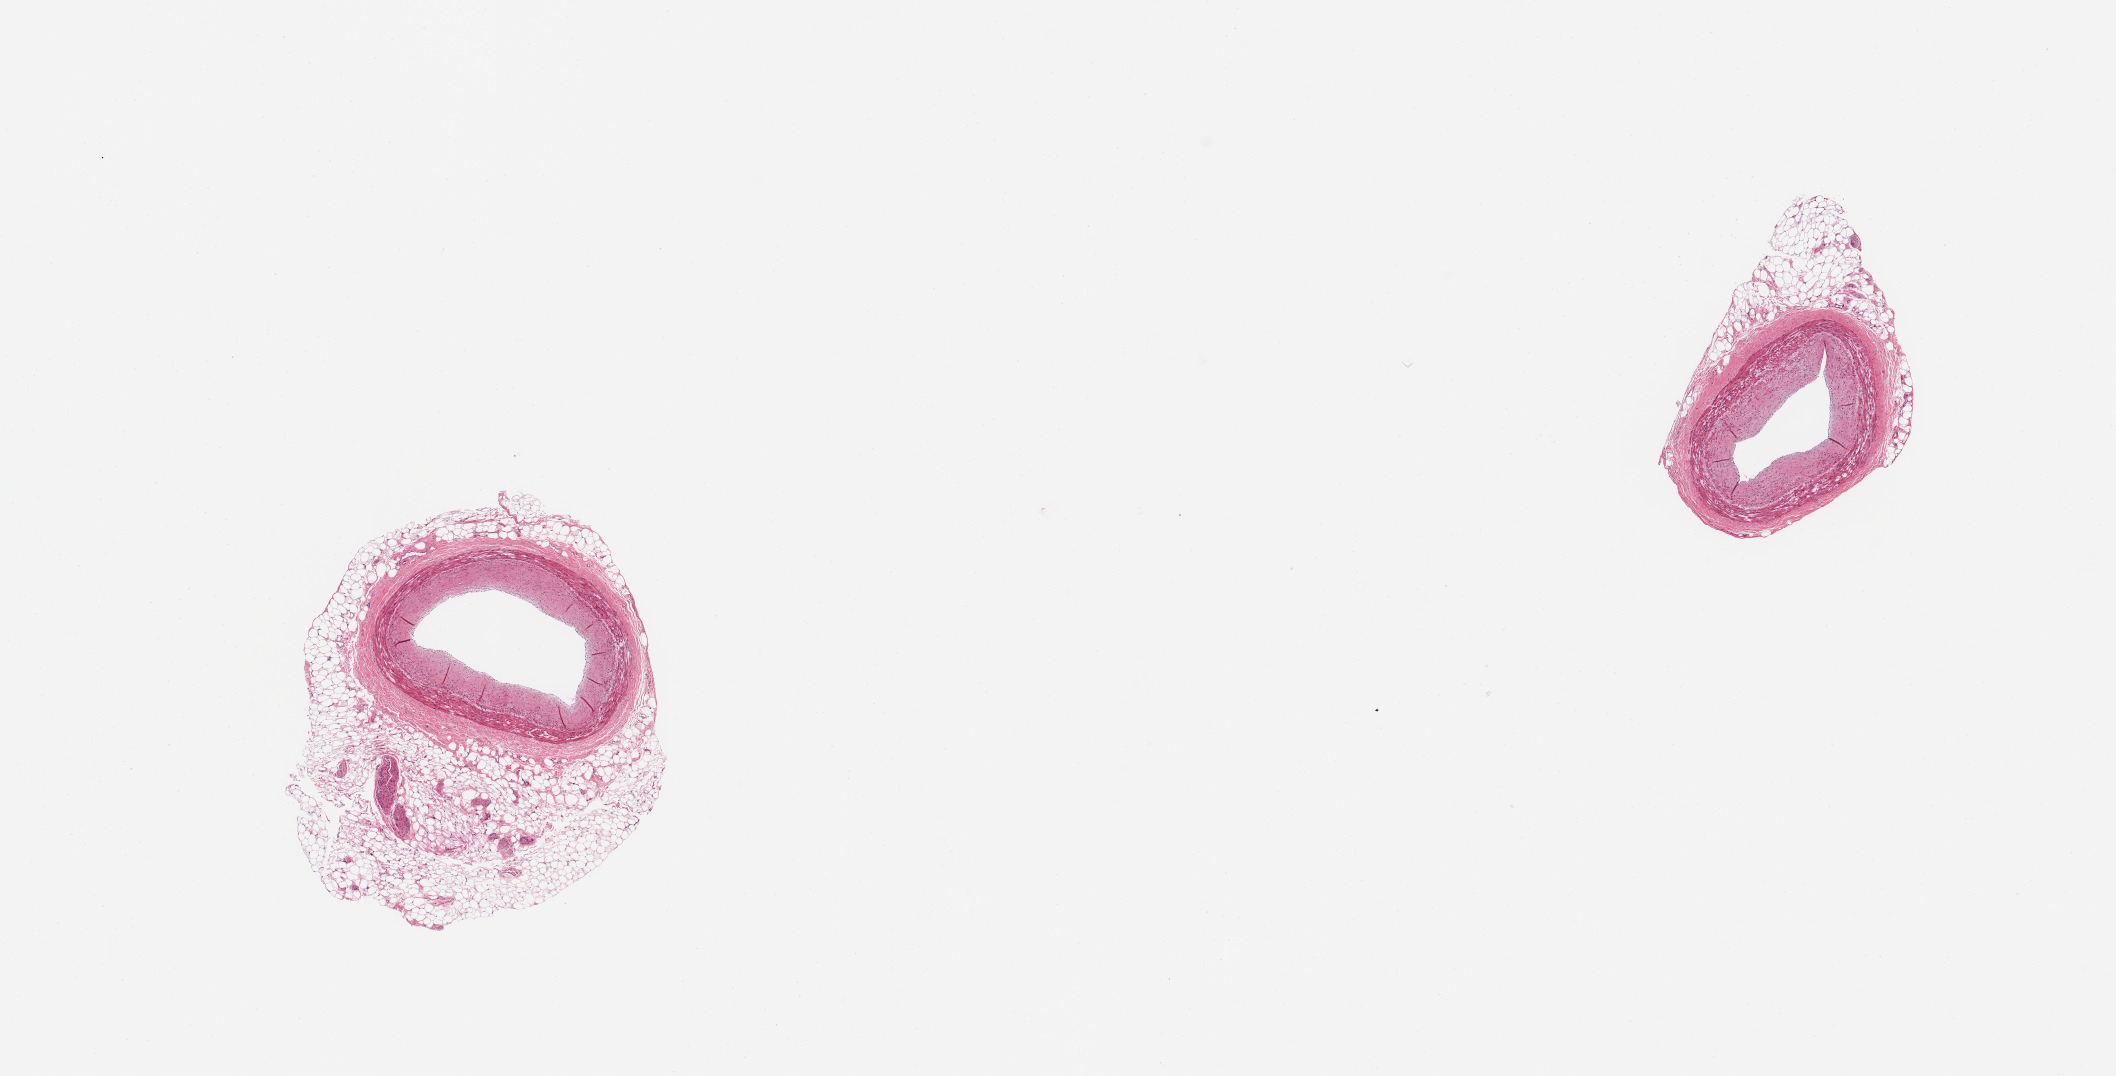
Digitized haematoxylin and eosin-stained section — a low-resolution overview of the entire scanned area, about 16.7 x 8.5 mm; PAXgene-fixed paraffin-embedded (PFPE) section; sampled site (target tissue): coronary artery; tissue donor sample.
Review note (as recorded): 2 pieces; concentric mild to moderate fibrous plaques.